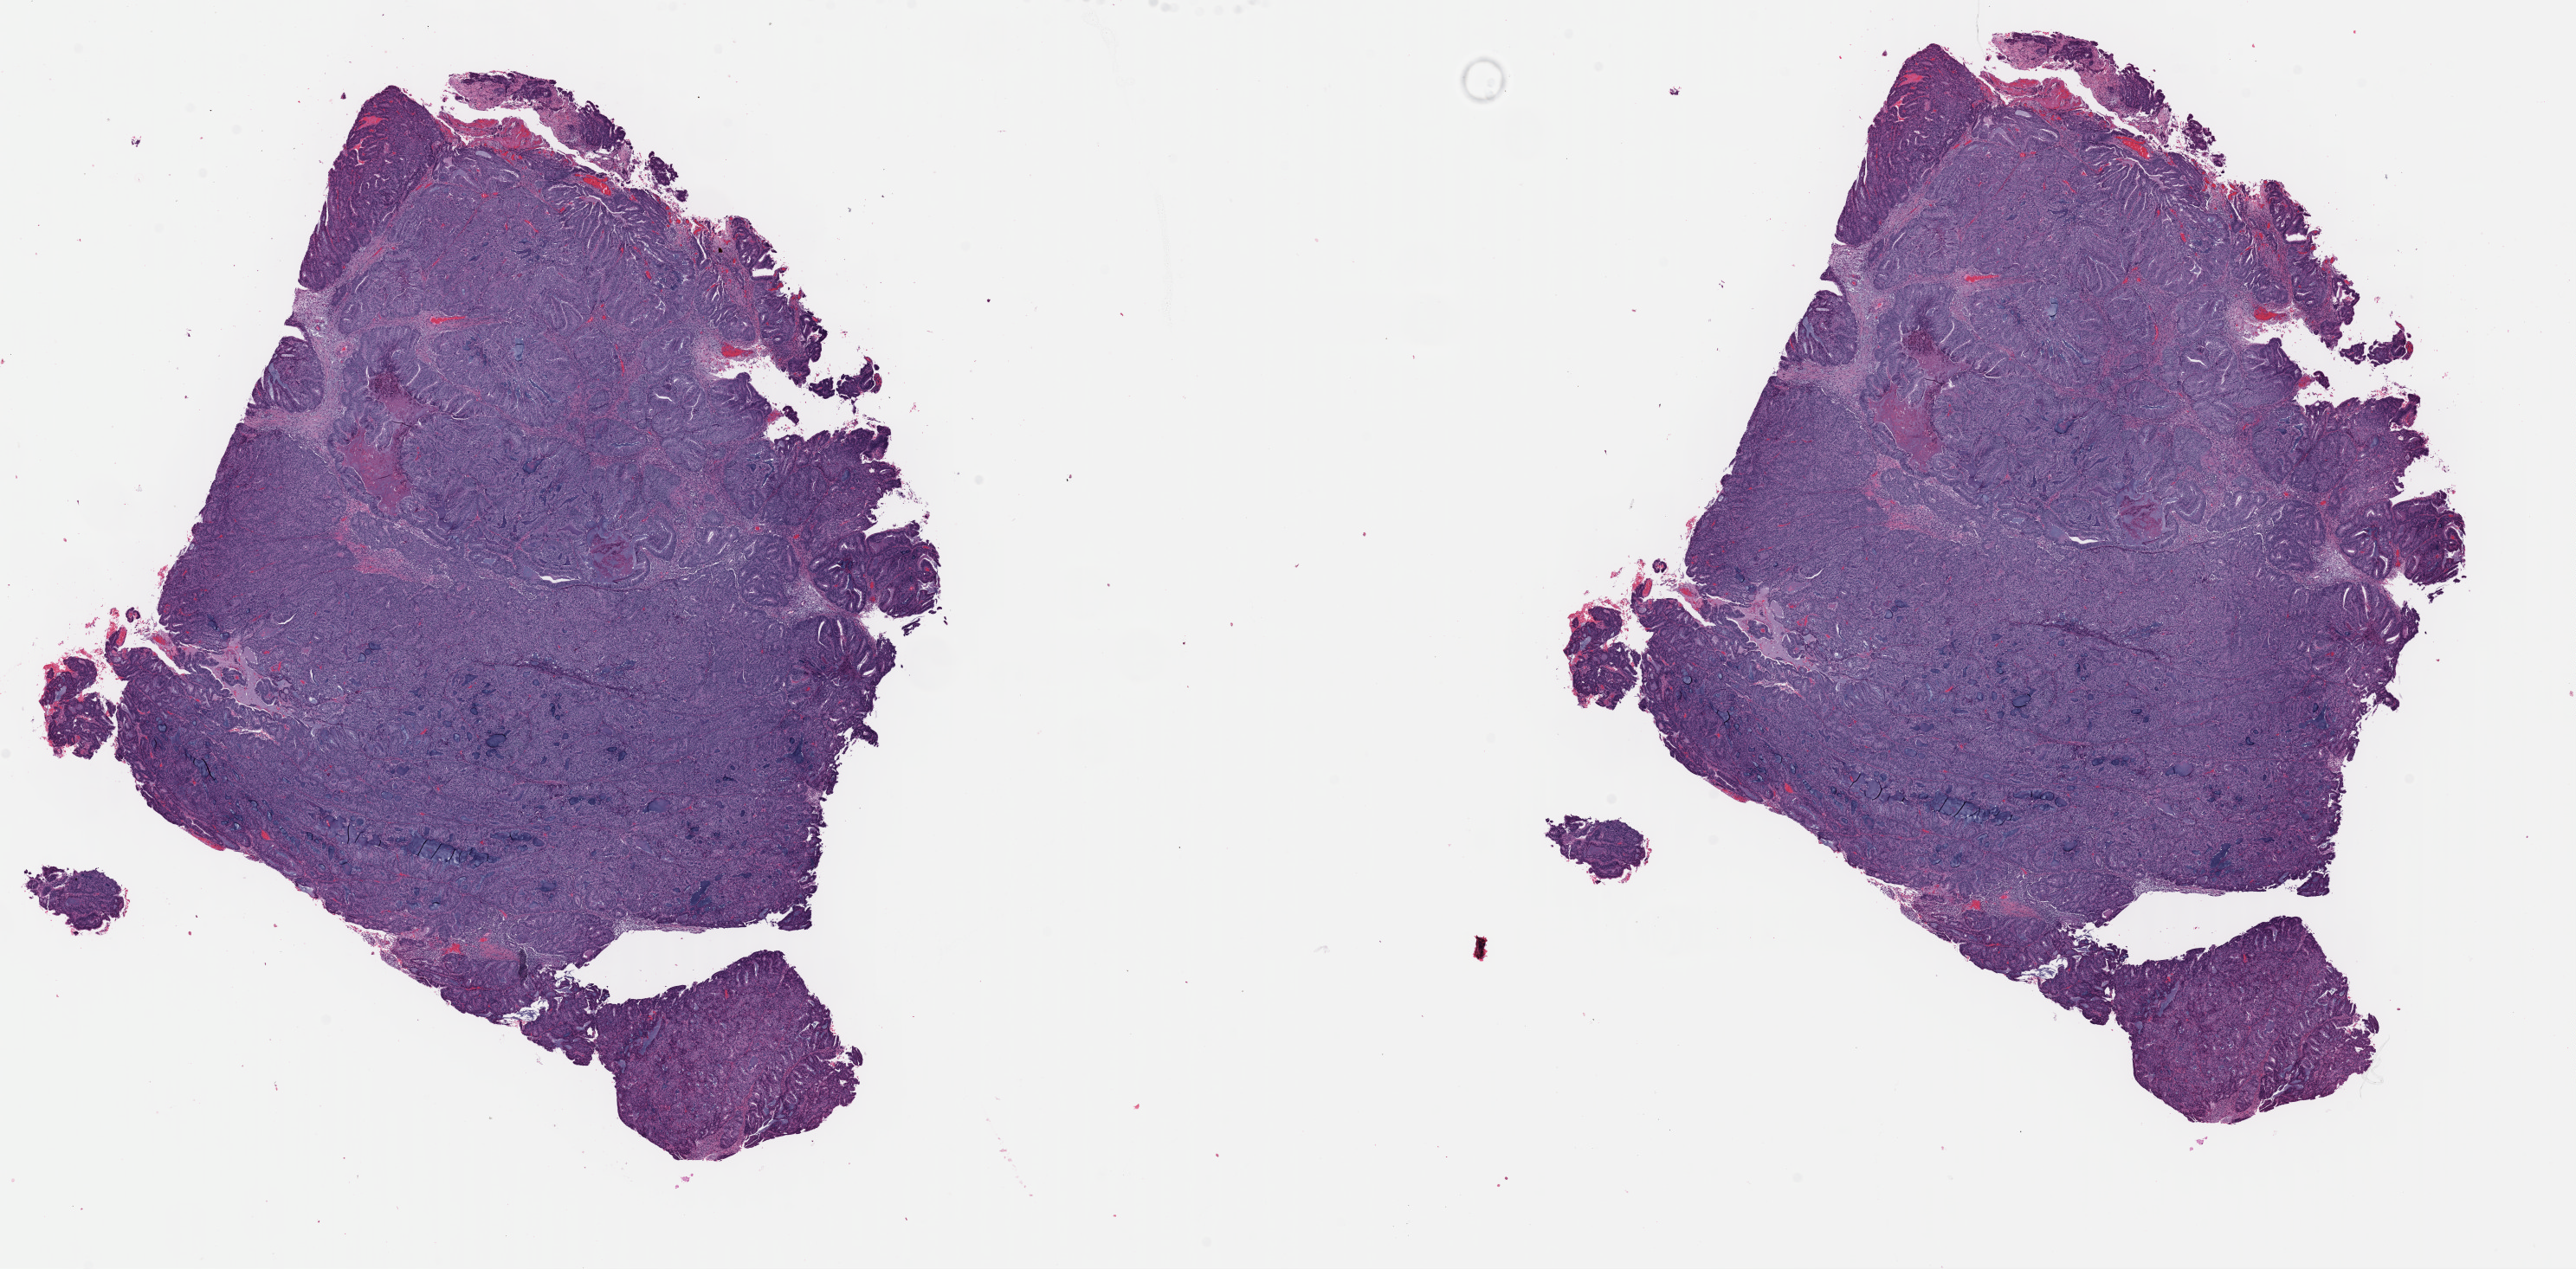
Digitized Hematoxylin and eosin (H&E) stained tissue section (whole slide), a low-resolution overview of the entire scanned area, about 23.5 x 11.6 mm (slide scanned at 40x); FFPE section; primary tumour sample from the uterus. Patient: female, age at initial diagnosis 75 years. Histologic grade: G2 (moderately differentiated).
FIGO stage: IA. Diagnosis: Endometrioid adenocarcinoma, NOS (endometrium).